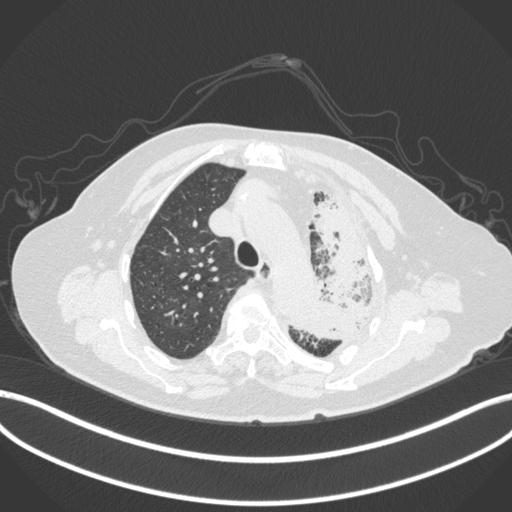
Chest CT, one axial slice. Position 296 of 399 along the scan axis. Reconstruction kernel B31f. Lung window (W 1500 / L -600 HU). 512 × 512 image matrix, field of view 400 × 400 mm. Female patient, age 75 years. From the clinical record (not read from this slice): clinical TNM (as recorded): T3 N3 M1.
Annotated regions visible in this slice (rectangle marked by the reading radiologist):
- lung tumour (recorded histology: adenocarcinoma): bounding box [x1, y1, x2, y2] px = [290, 198, 387, 347]